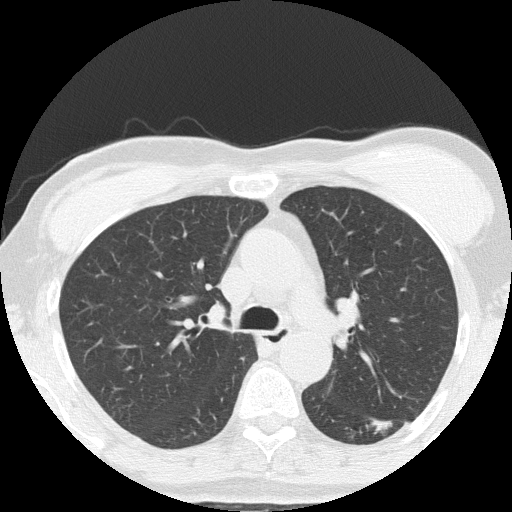
Axial slice from a low-dose chest CT screening exam. Third screening round (two years after baseline). Lung window (W 1500 / L -600 HU). 2 mm slice thickness. 120 kVp. Slice 53 of 152 in the series. 512 × 512 image matrix. Female, age 64 years at enrolment. Former smoker at enrolment.
Expert-annotated lung lesion, box from (x=339, y=393) to (x=425, y=460) px. The screening reader recorded 3 non-calcified nodules or masses ≥4 mm on this exam (right upper lobe, left lower lobe, right middle lobe); which of them this box marks is not recorded. Official screen result: positive, other. Later outcome: lung cancer diagnosed 212 days after this screen — adenocarcinoma, NOS, left lower lobe, moderately differentiated (G2), stage IA (AJCC 6th edition), 17 mm at pathology.